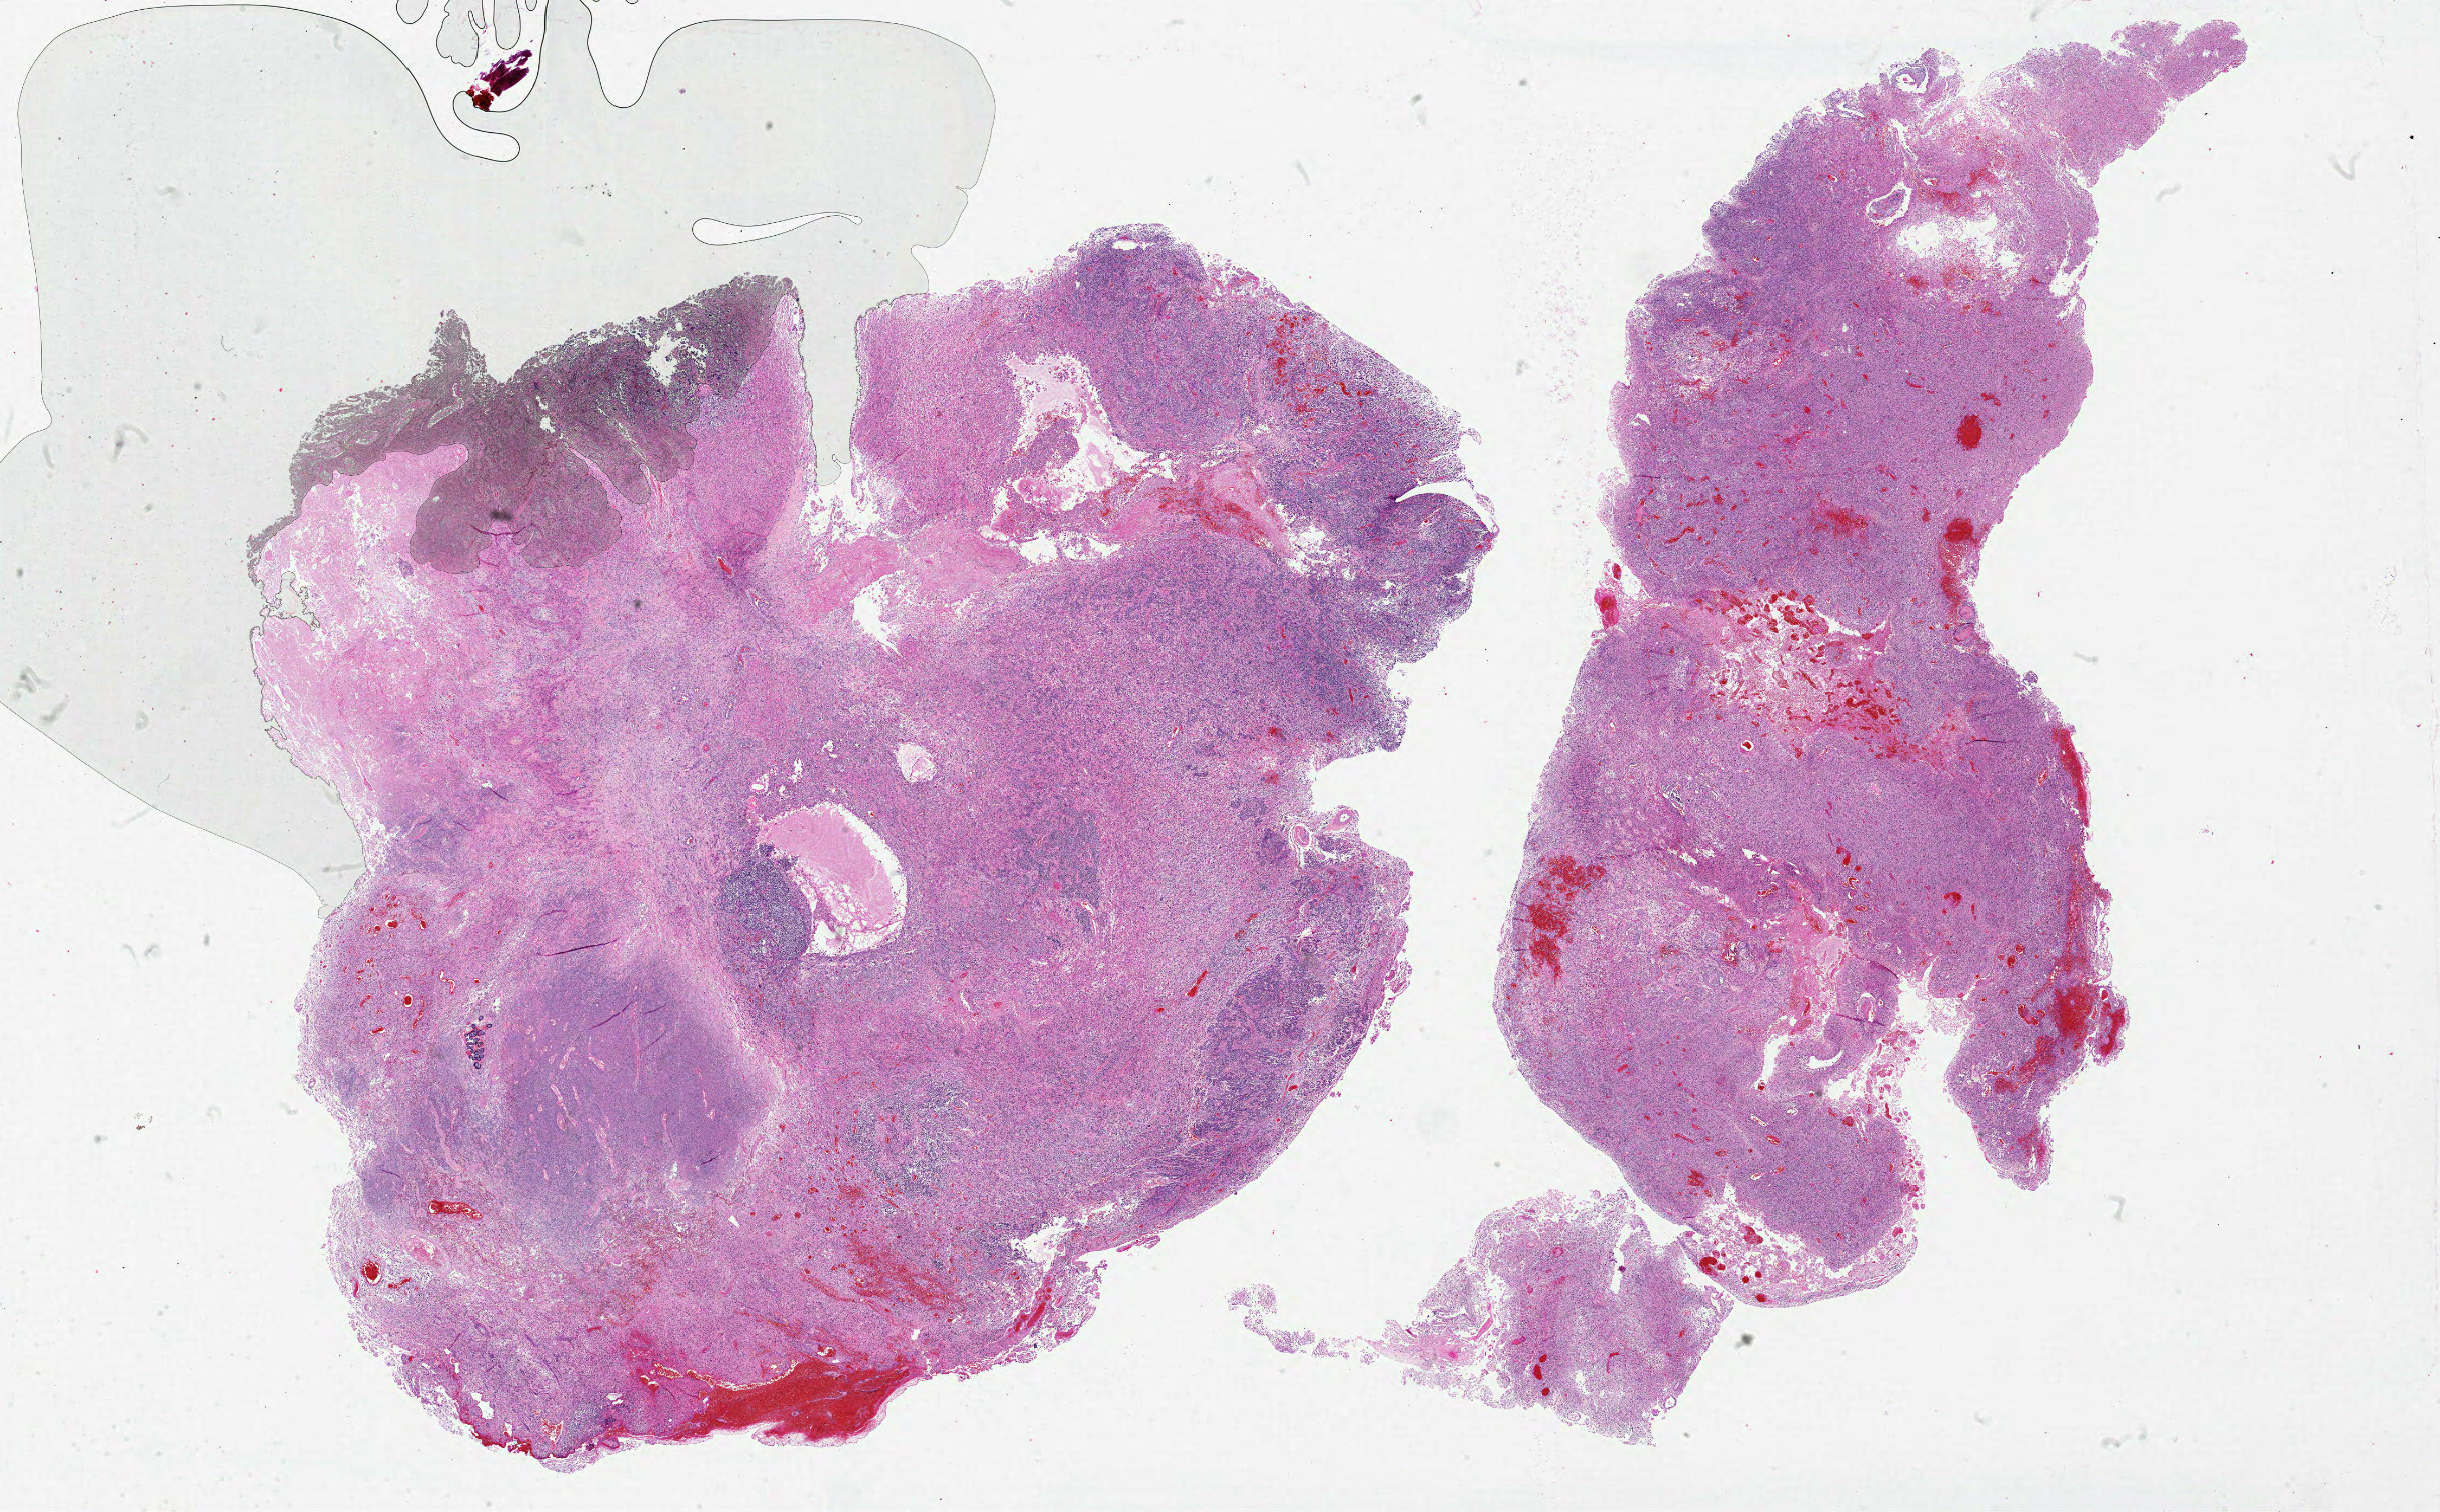
Whole-slide histology image, H&E-stained — a low-resolution overview of the entire scanned area, about 36.0 x 22.3 mm, formalin-fixed paraffin-embedded (FFPE) diagnostic section, sample: primary tumour, brain. Patient: male, age at initial diagnosis 60 years.
Histologic diagnosis: Glioblastoma.